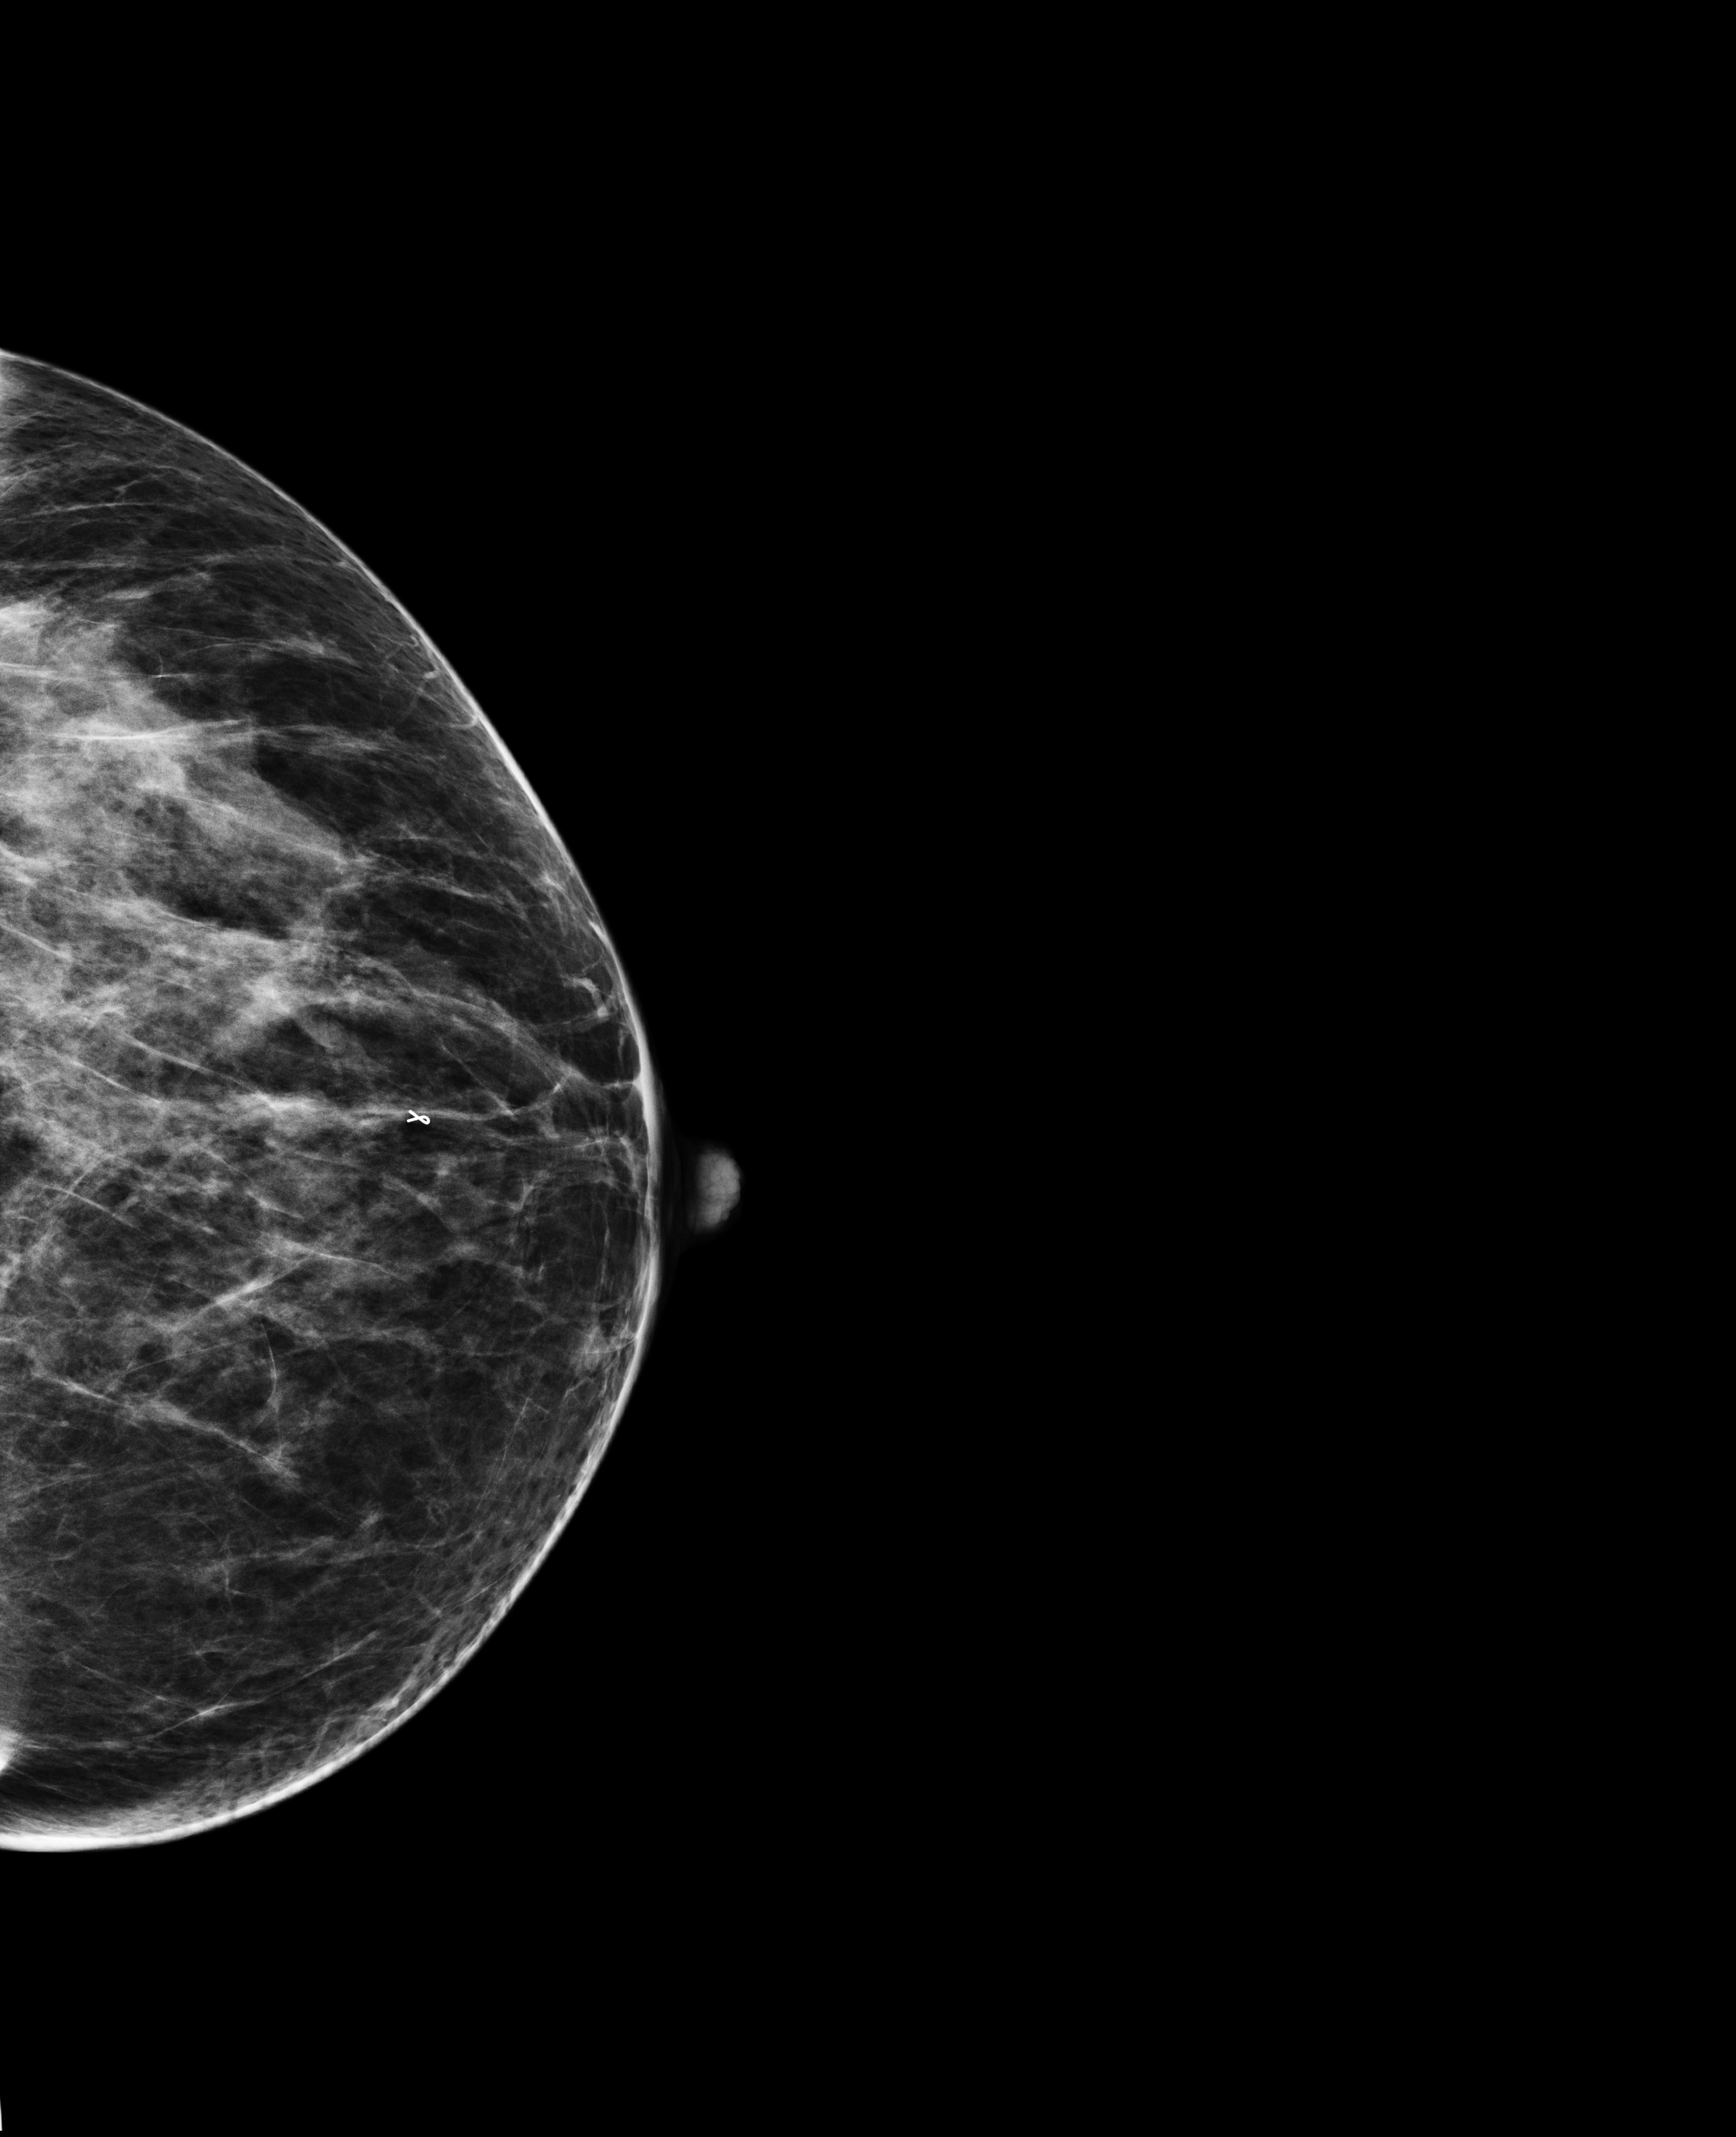
Annual screening mammography examination, compressed breast thickness 60 mm, system: Selenia Dimensions.
Image type: full-field digital mammogram. Breast: left. Projection: cranio-caudal projection.